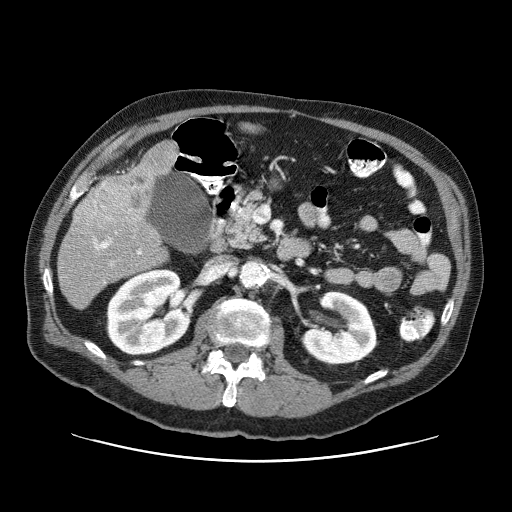
Contrast-enhanced abdominal CT (liver protocol), one axial slice; slice 25 of 87 in the series (ordered by position); reconstruction kernel STANDARD; 120 kVp; one of 3 acquisitions stored at this slice position; soft-tissue window (W 400 / L 40 HU); 512 × 512 image matrix, field of view 400 × 400 mm. Case-level facts recorded for this patient, not image findings: diagnosis: hepatocellular carcinoma (patient treated with transarterial chemoembolisation; whether this scan precedes or follows treatment is not stated here); TNM stage (as recorded): Stage-IIIA; Child-Pugh class: A; tumour differentiation: well differentiated.
Structures marked on this image (semi-automatic segmentation, software-assisted and operator-edited):
- liver parenchyma outside the tumour (the mass and vessels are separate outlines, so this box may not span the whole liver): box from (x=58, y=142) to (x=178, y=308) px
- mass: (x=74, y=168)–(x=156, y=233)
- liver vessels: (x=94, y=218)–(x=142, y=265)